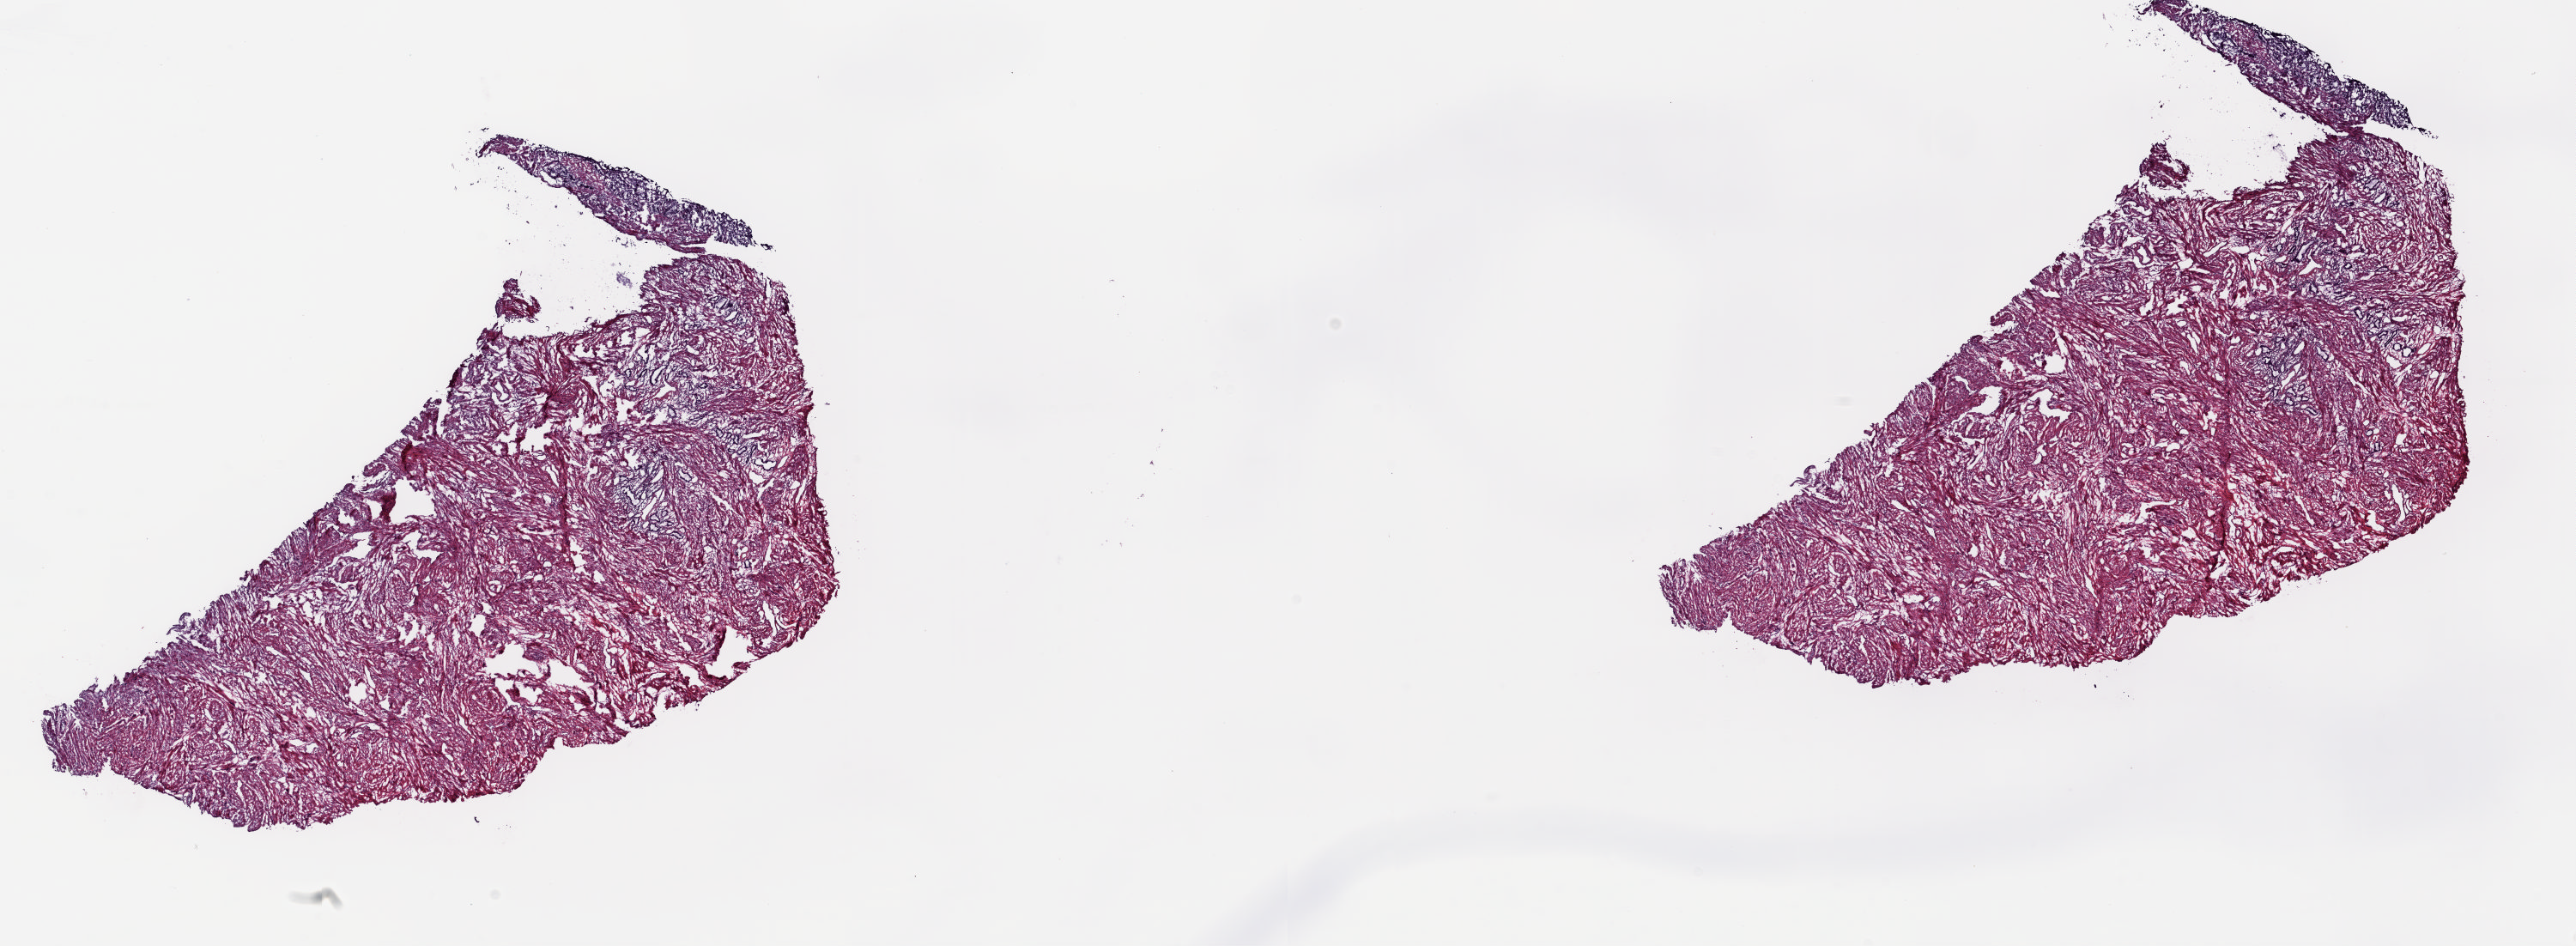
Whole-slide histology image, Hematoxylin and eosin (H&E) stained, whole scanned area (about 23.8 x 8.7 mm) shown as a low-resolution overview; frozen section from the top of the tissue portion; sample: solid tissue normal (non-tumour tissue), uterus. Slide review estimates, as recorded: tumour cells 0%, tumour nuclei 0%, normal cells 30%, stromal cells 70%, necrosis 0%. Infiltration values recorded for this section: lymphocyte infiltration 0%, monocyte infiltration 0%, neutrophil infiltration 0%.
This section: solid tissue normal sample (biorepository sample class).